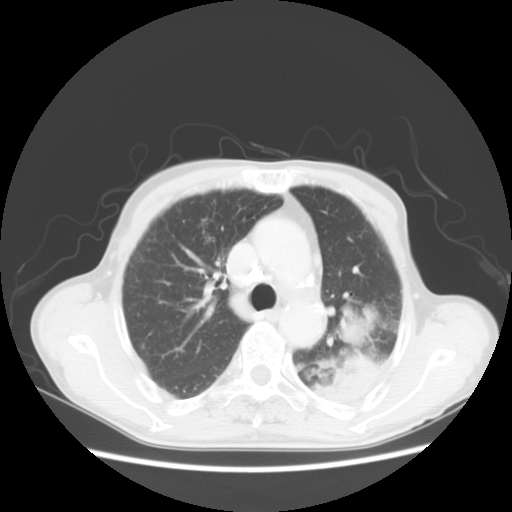
Chest CT, one axial slice. Position 37 of 51 along the scan axis. Reconstruction kernel STANDARD. Lung window (W 1500 / L -600 HU). 512 × 512 image matrix. Patient: male, 64 years. From the clinical record (not read from this slice): clinical TNM (as recorded): T4 N0 M0; histopathological grade: G2-3.
Annotated regions visible in this slice (rectangle marked by the reading radiologist):
- lung tumour (recorded histology: squamous cell carcinoma): bounding box <326,309,378,399> (left, top, right, bottom; pixels)